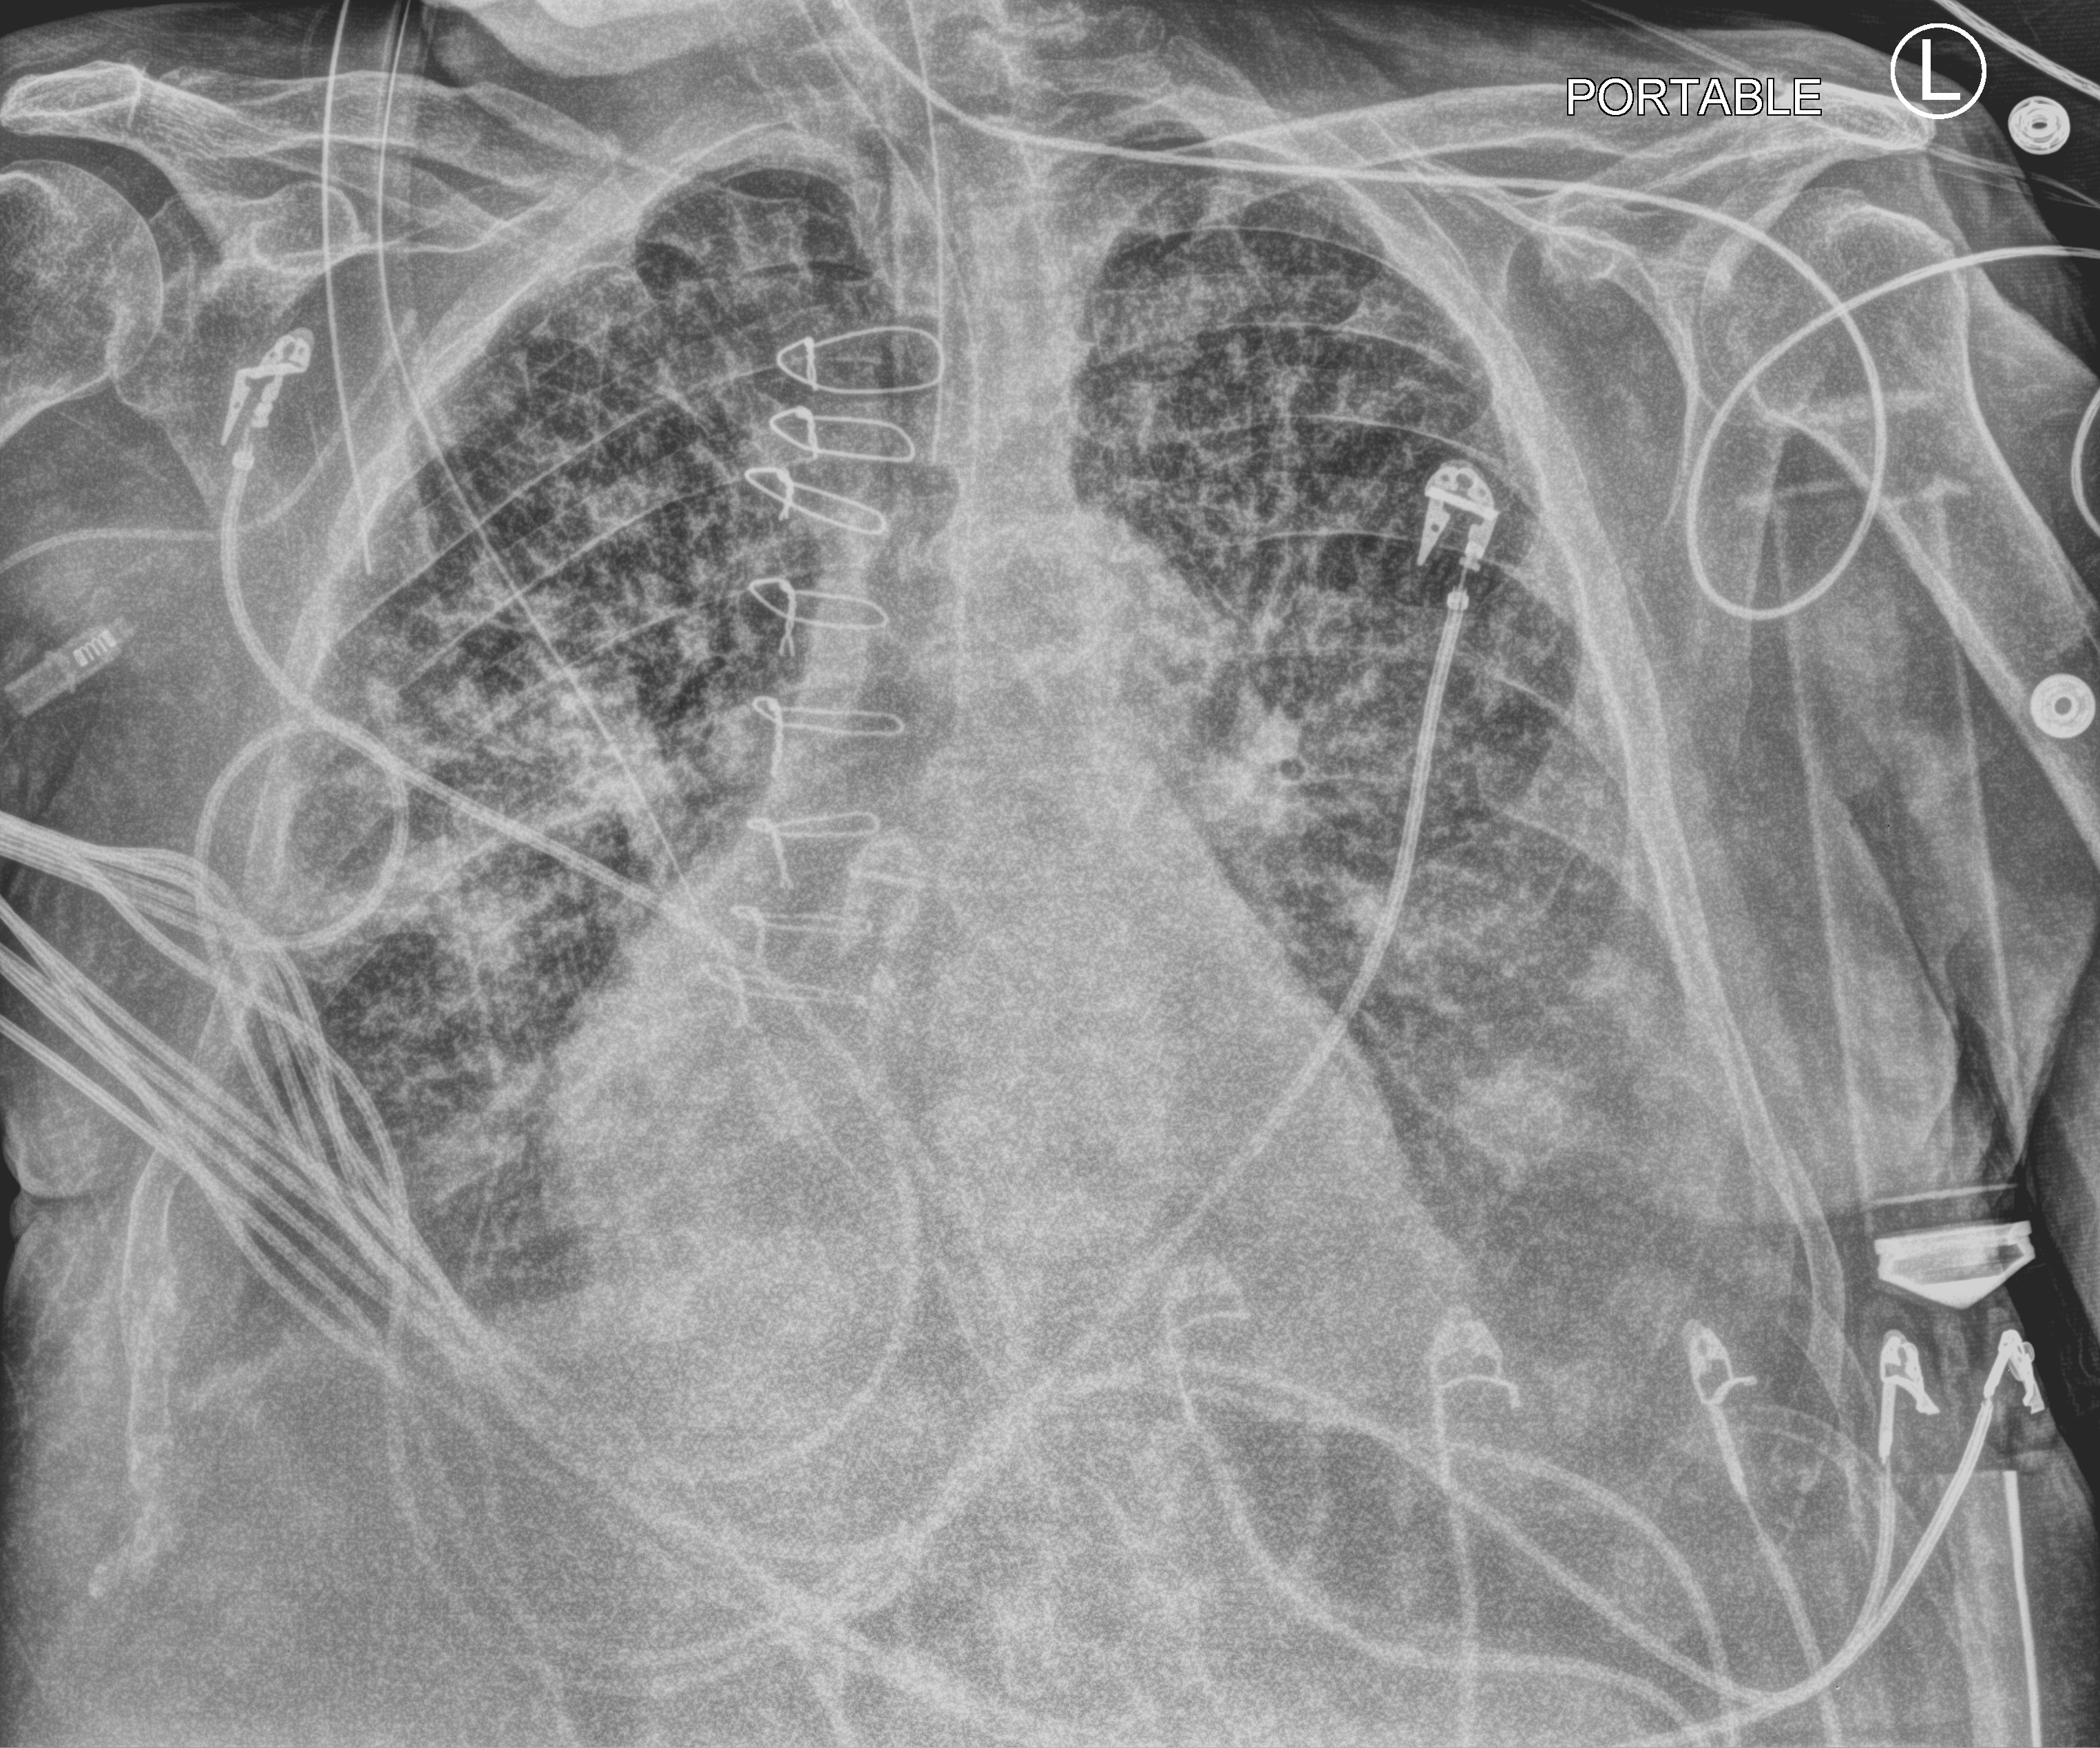
Bedside chest radiograph (computed radiography); anteroposterior (AP) projection. Patient hospitalised with COVID-19; male, aged 75–90 years.
From the hospital-stay record, not from the radiograph (when in the stay this image was taken is not recorded):
- admitted to intensive care during this hospital stay: yes
- mechanically ventilated during this hospital stay: yes
- length of hospital stay: 40 days